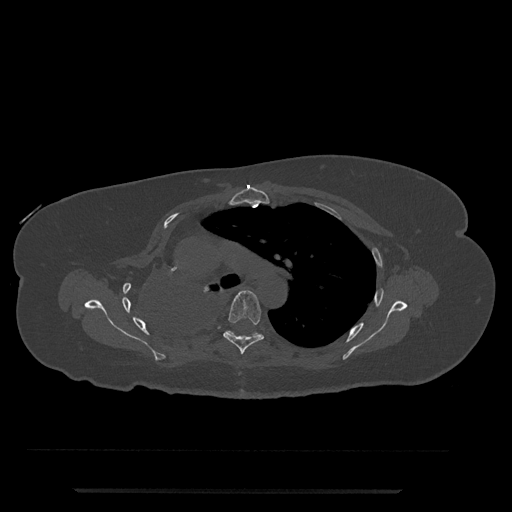
CT including the spine, one axial slice. Slice 539 of 797 in the series (ordered by position). Reconstruction kernel Br40s/3. 120 kVp. Bone window (W 1800 / L 400 HU). 0.5 mm slice thickness. 512 × 512 image matrix, field of view 440 × 440 mm. Female patient, age 51 years. From the clinical record (not read from this slice): primary cancer: neuro.
Outlined on this slice (semi-automatic segmentation, software-assisted and operator-edited):
- T5 vertebra: bounding box <223,290,264,355> (left, top, right, bottom; pixels)
- T6 vertebra: <226,331,258,336>